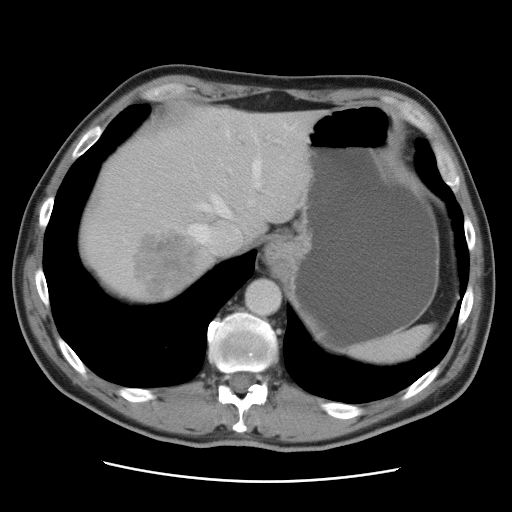
Contrast-enhanced abdominal CT, one axial slice. Position 74 of 89 along the scan axis. 120 kVp. Soft-tissue window (W 400 / L 40 HU). 5 mm slice thickness. 512 × 512 image matrix, field of view 366 × 366 mm. Male patient, age 59 years. Case-level facts recorded for this patient, not image findings: diagnosis: colorectal cancer liver metastases, imaged before liver resection; multiple liver metastases: yes; largest metastasis: 0.6 cm; chemotherapy before resection: no.
Outlined on this slice (expert manual segmentation):
- hepatic veins: box from (x=137, y=124) to (x=294, y=256) px
- liver: (x=78, y=108)–(x=320, y=305)
- planned liver remnant (the part of the liver to remain after resection): (x=124, y=108)–(x=320, y=244)
- portal vein (with intrahepatic branches): (x=276, y=140)–(x=278, y=142)
- liver metastasis: (x=137, y=235)–(x=207, y=303)